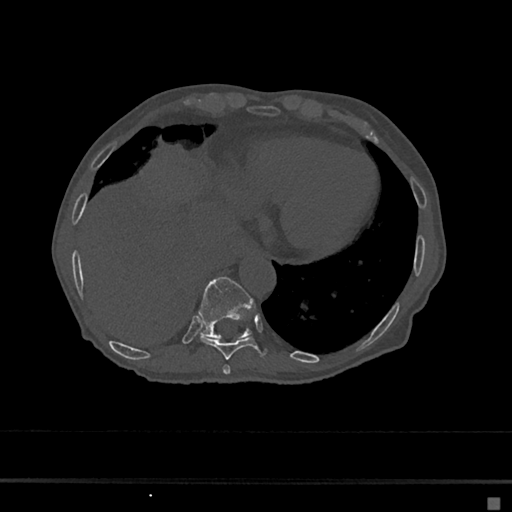
CT including the spine, one axial slice; position 255 of 797 along the scan axis; reconstruction kernel Br40s/3; bone window (W 1800 / L 400 HU); 0.5 mm slice thickness; 512 × 512 image matrix, field of view 360 × 360 mm. Patient: female, 68 years. From the clinical record (not read from this slice): primary cancer: renal.
Structures marked on this image (semi-automatic segmentation, software-assisted and operator-edited):
- T10 vertebra: bounding box <199,277,253,339> (left, top, right, bottom; pixels)
- T8 vertebra: <222,364,231,375>
- T9 vertebra: <200,336,267,360>